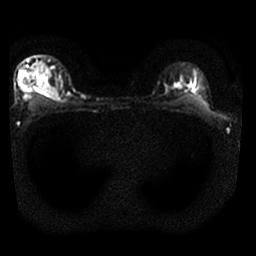
Breast MRI, one axial slice; slice 23 of 25 in the series (ordered by position); diffusion-weighted series; image 2 of 4 stored at this slice position (different b-values; order by instance number); 1.5 T; 4 mm slice thickness; 256 × 256 image matrix. Female patient.
Outlined on this slice (expert manual segmentation):
- tumour on diffusion-weighted imaging: box from (x=38, y=79) to (x=58, y=96) px